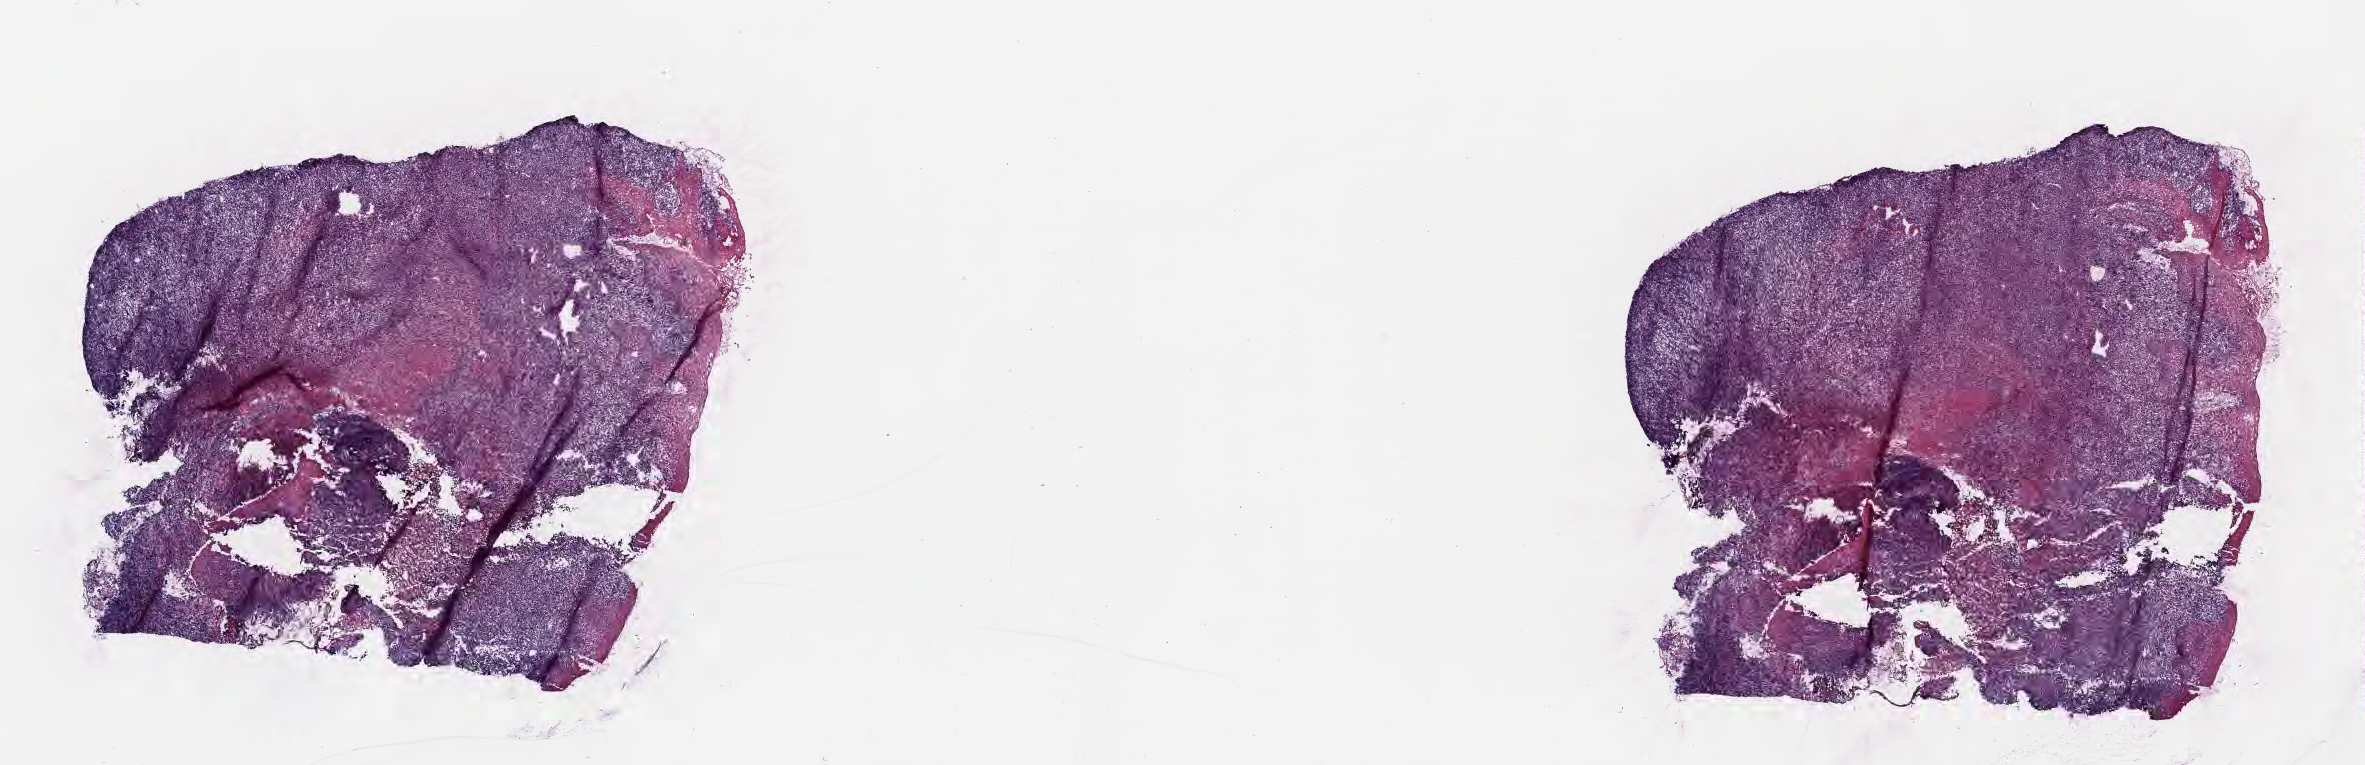
Digitized H&E-stained section — low-resolution overview of the scanned area, about 19.1 x 6.2 mm. Frozen section (tissue freezing medium). Primary tumor. Anatomic site: cranium. Male patient, age 11 years. Composition of this section per pathologist review: tumor cells 70%, tumor nuclei 75%, stromal cells 20%, necrosis 0%, normal cells 10%. Infiltration values recorded for this section: lymphocyte infiltration 40%, monocyte infiltration 20%, neutrophil infiltration 5%.
• section: top of the tissue portion
• Ann Arbor stage (patient): Stage III
• histologic diagnosis: Diffuse large B-cell lymphoma, NOS